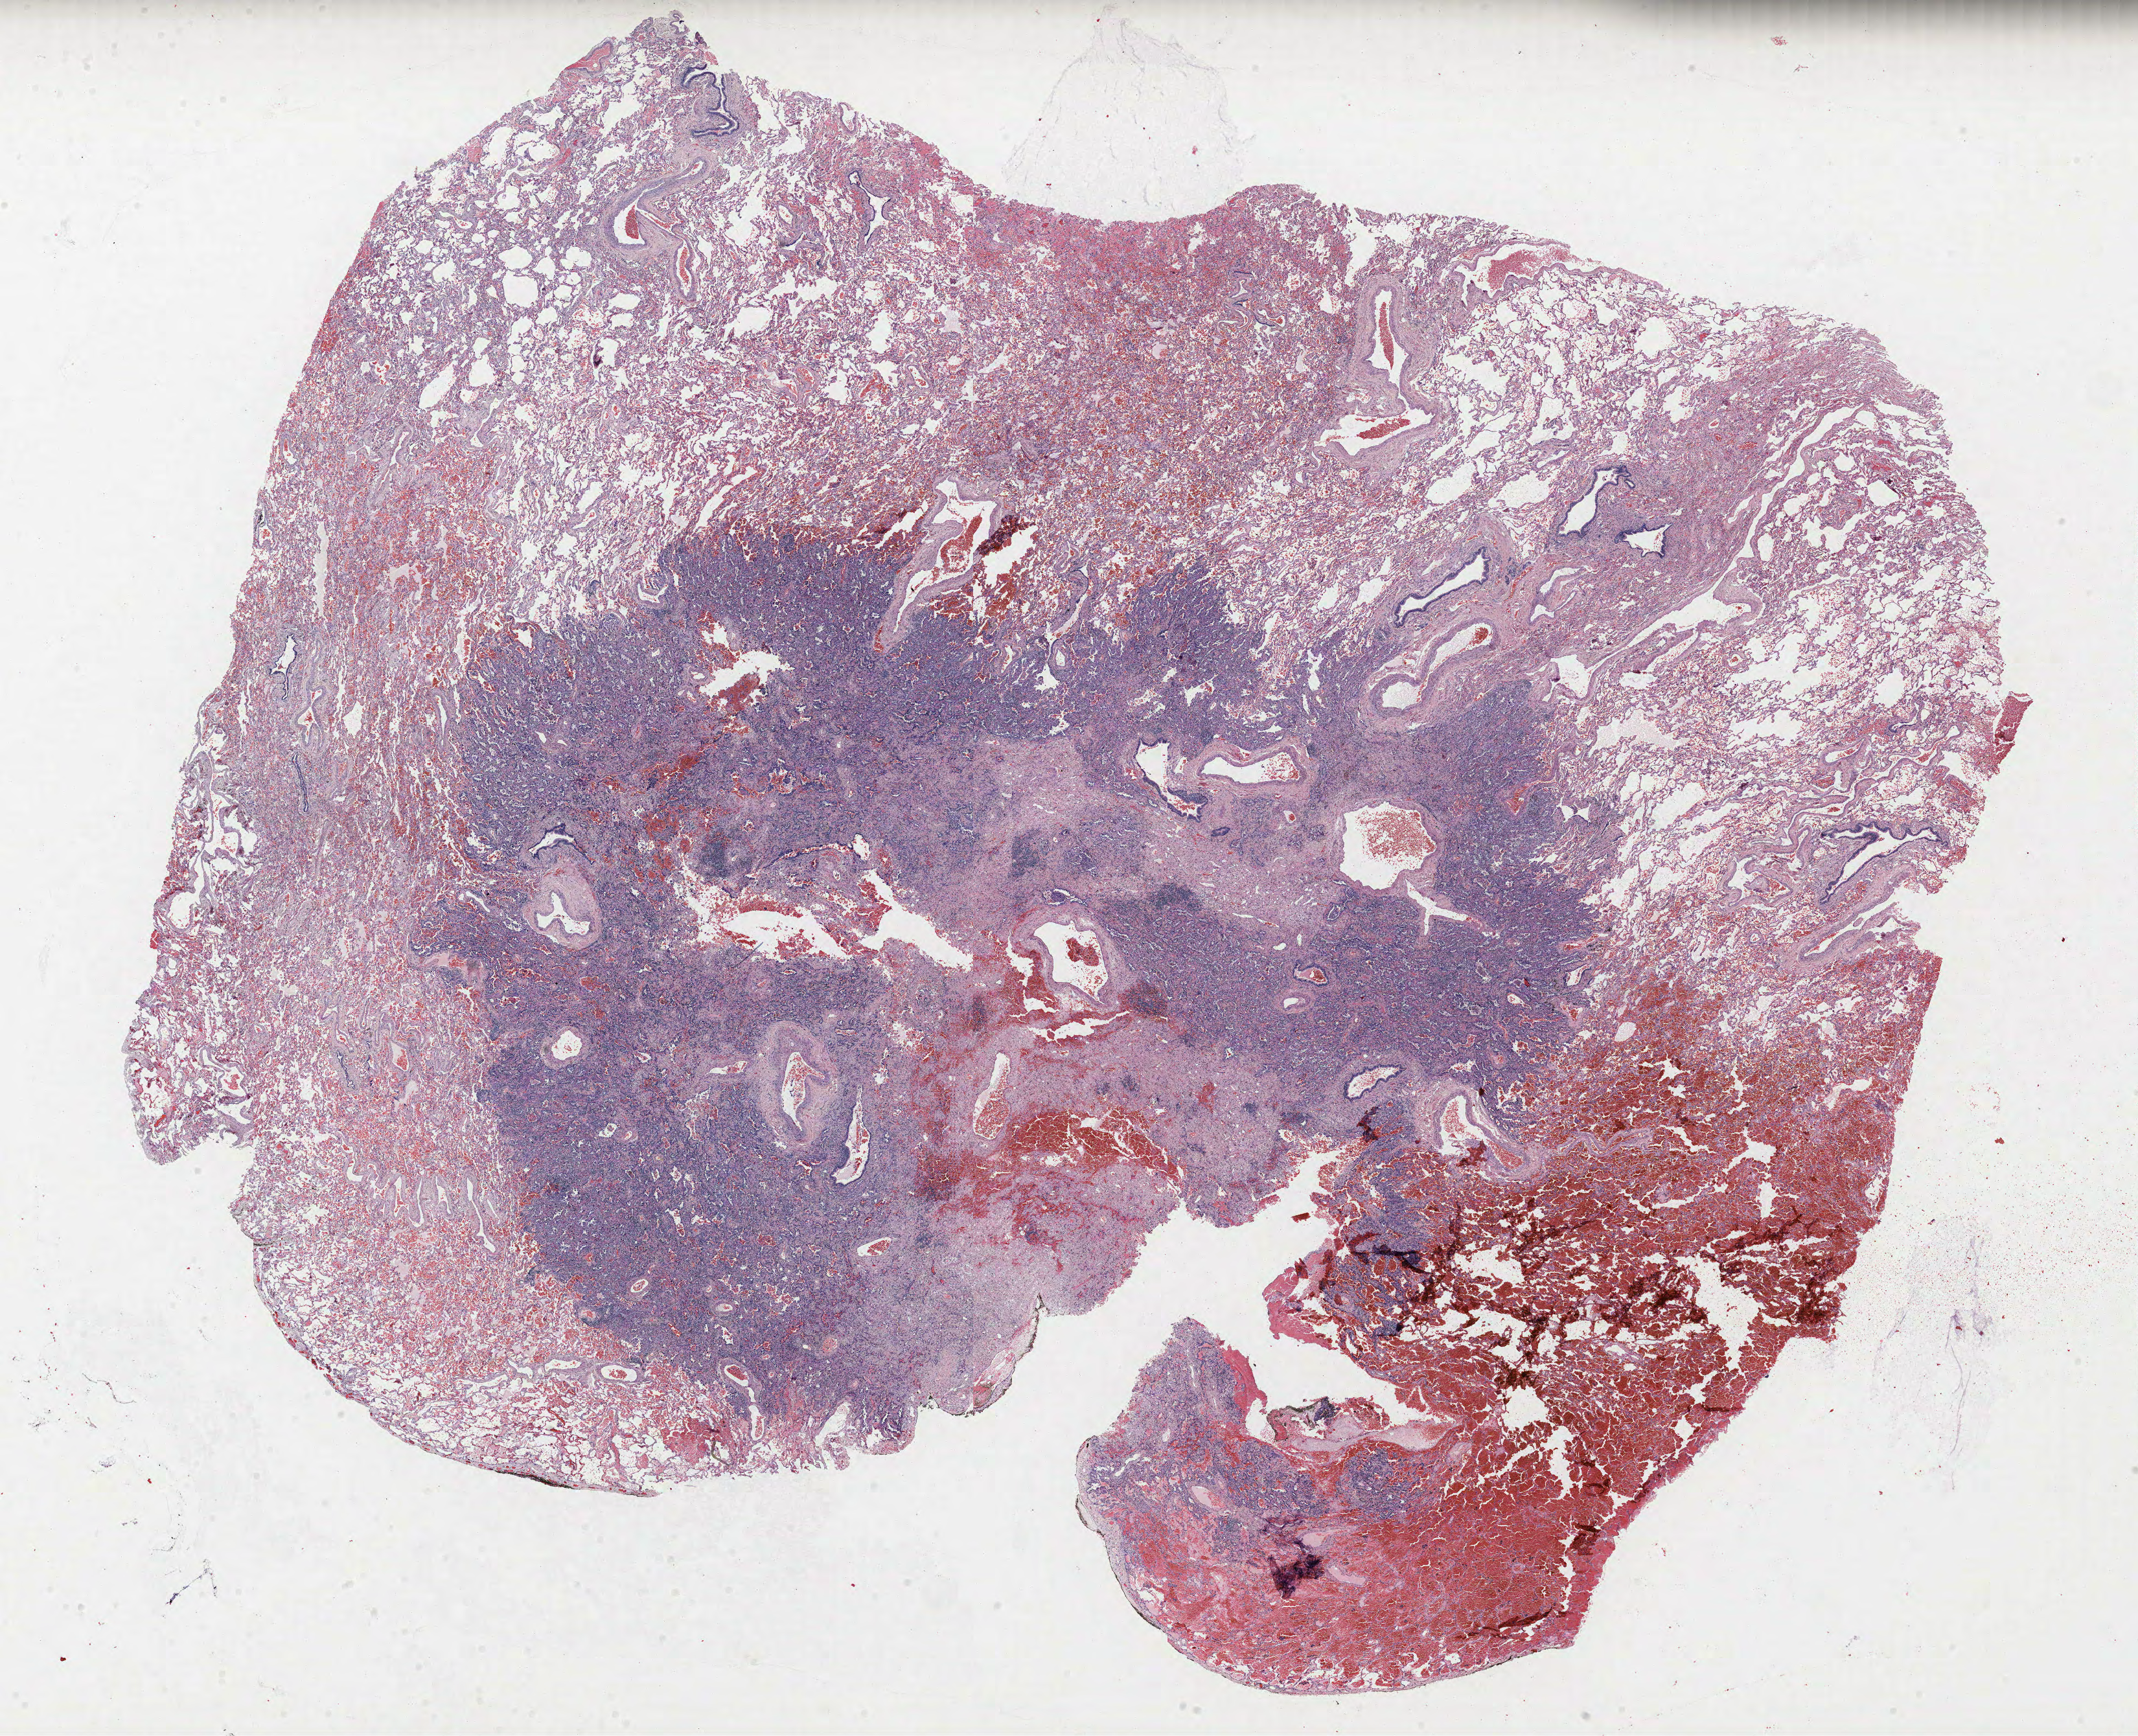
Hematoxylin and eosin (H&E) stained whole-slide image — low-resolution overview of the scanned area, about 26.4 x 21.4 mm, formalin-fixed paraffin-embedded (FFPE) section, lung. Female patient, aged 59 at enrolment. Grade: well differentiated (G1).
Stage (AJCC 6th edition): IB. Tumour size (pathology): 20 mm. Primary tumour location (clinical record): right middle lobe. Participant's lung-cancer diagnosis: Bronchiolo-alveolar carcinoma, non-mucinous.